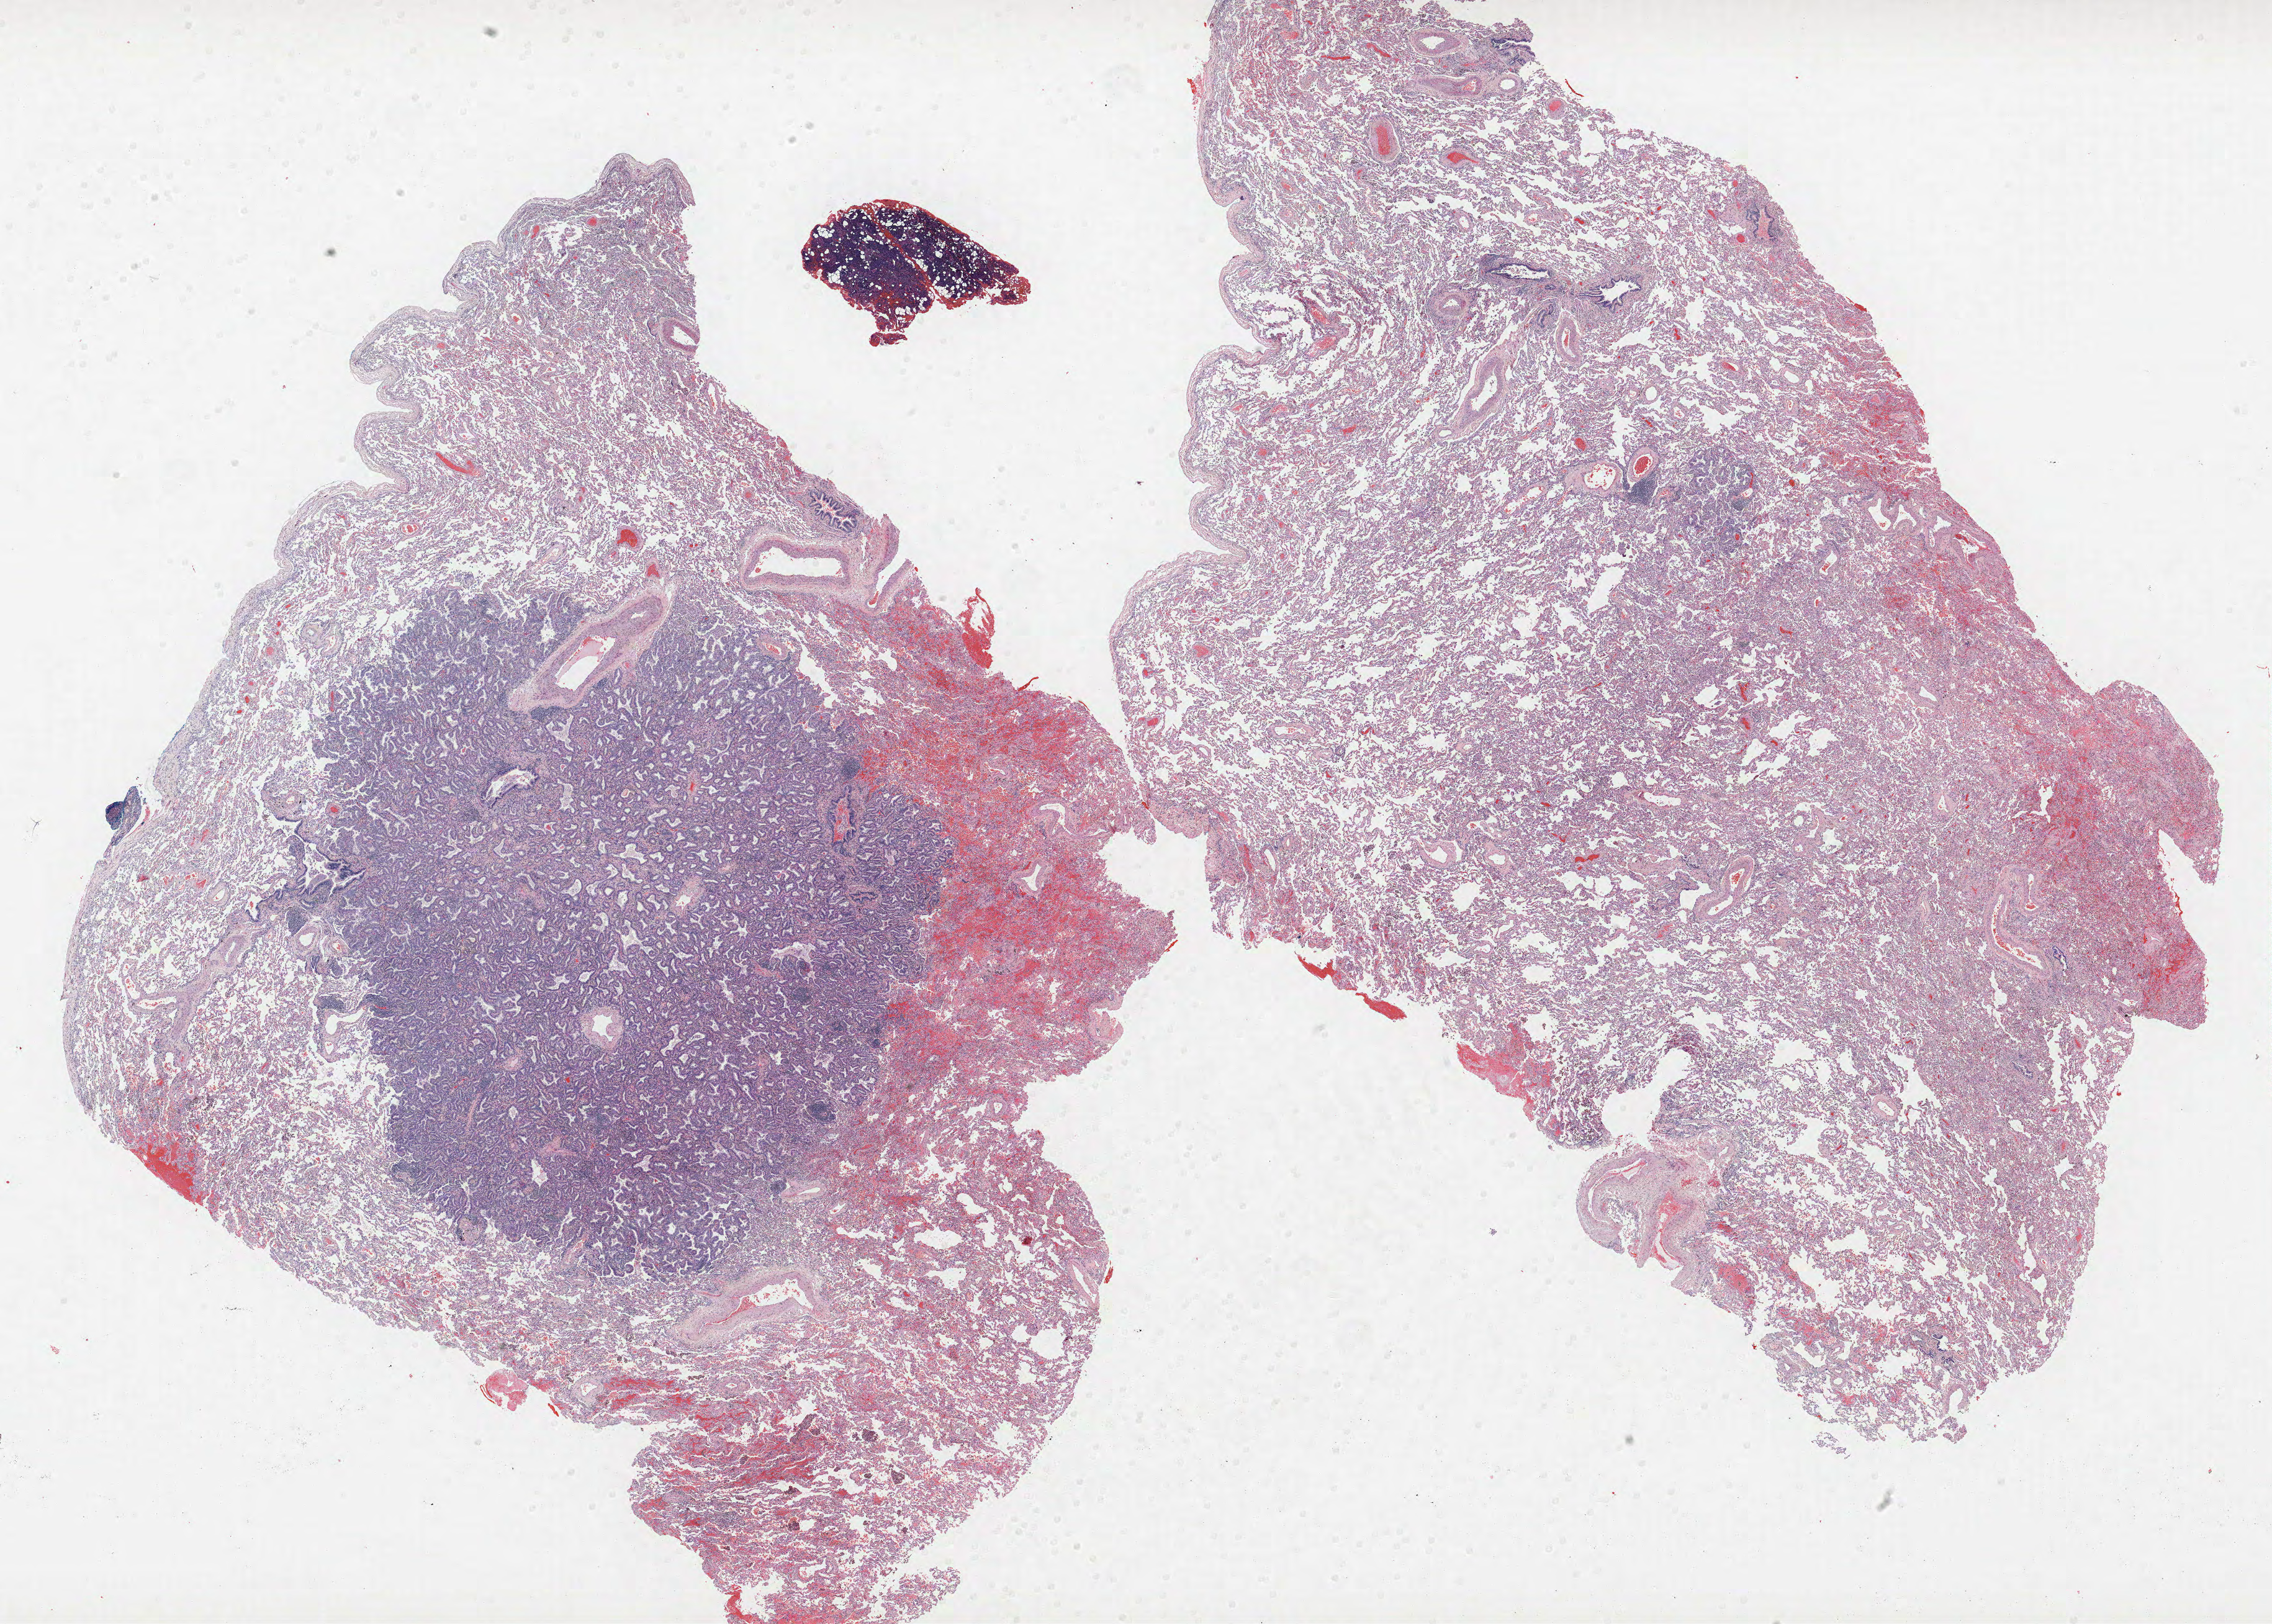
Whole-slide histology image, H&E-stained, whole scanned area (about 29.3 x 20.9 mm, acquisition: 40x scan) shown as a low-resolution overview. Formalin-fixed paraffin-embedded (FFPE) section. Lung. Female, age 72 at enrolment. Former smoker at enrolment. Grade: well differentiated (G1).
Tumour size (pathology): 9 mm. Primary tumour location (clinical record): left upper lobe. Stage (AJCC 6th edition): IA. Participant's lung-cancer diagnosis: Bronchiolo-alveolar adenocarcinoma, NOS.